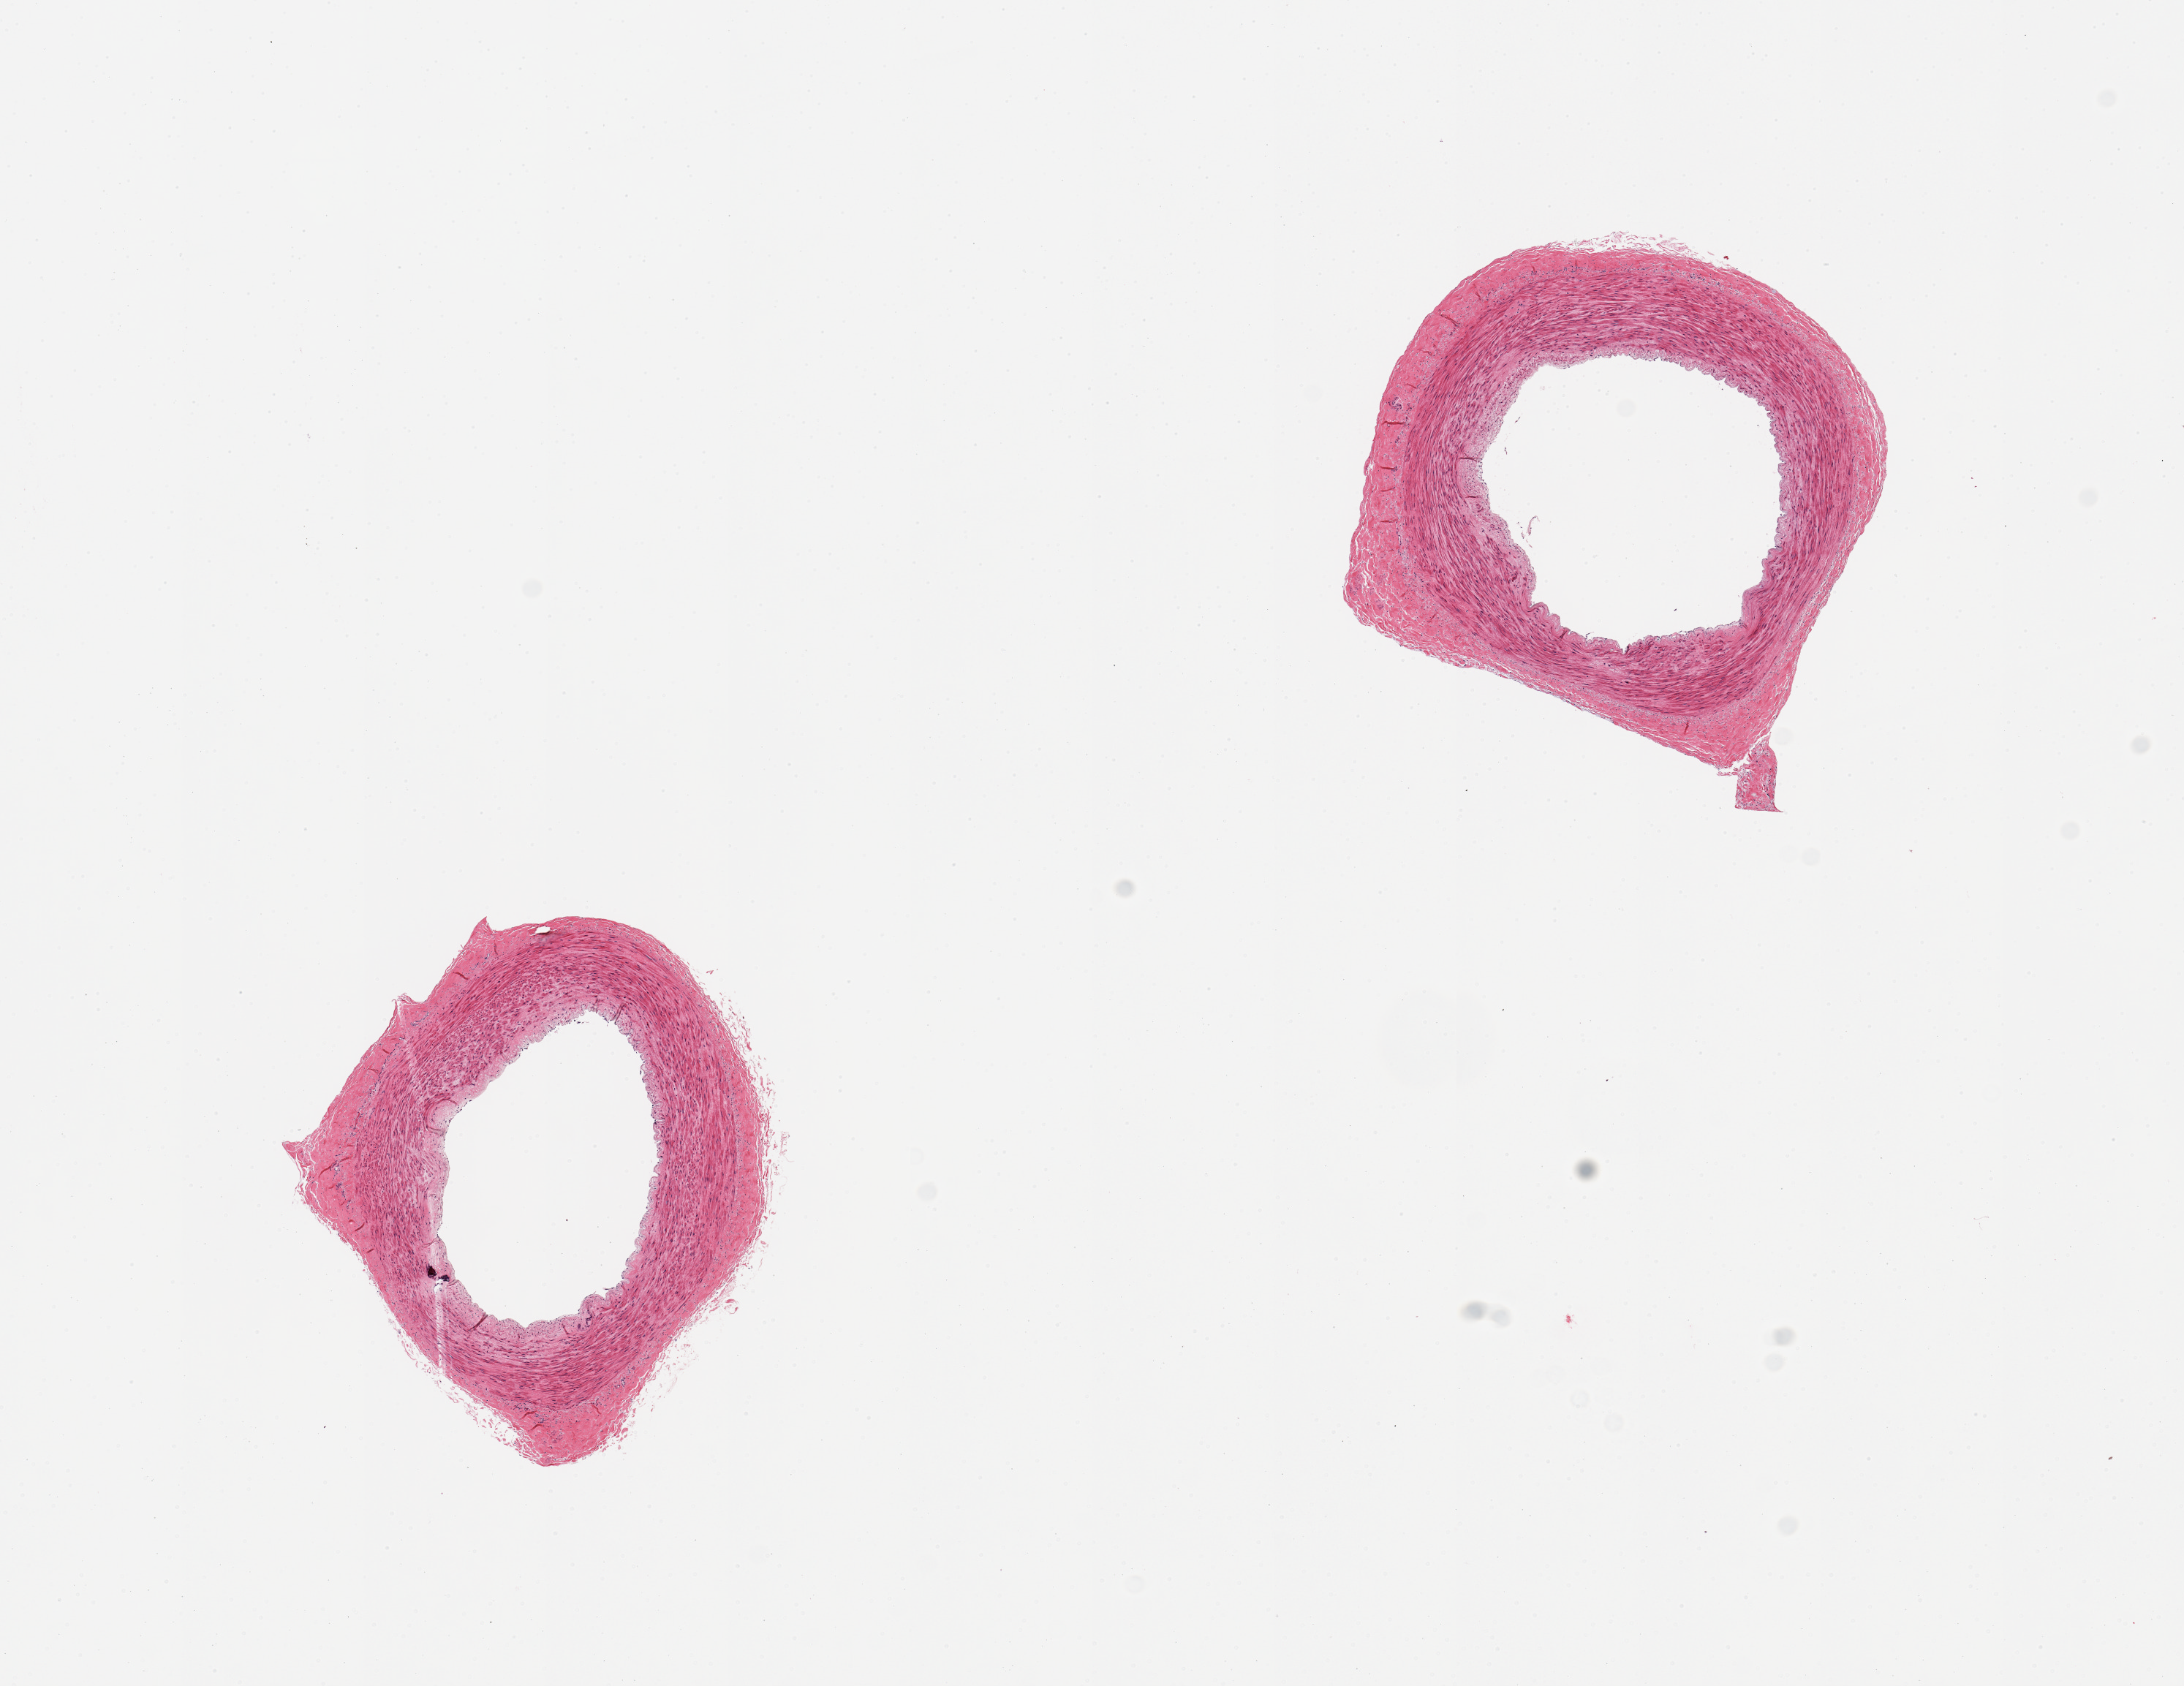
Hematoxylin and eosin (H&E) whole-slide image, brightfield — low-resolution overview of the scanned area, about 11.8 x 9.1 mm; PAXgene-fixed paraffin-embedded (PFPE) section; sampled site (target tissue): tibial artery; donor tissue sample. Donor: male.
Reviewer comment on this tissue sample: 2 pieces; no plaques.